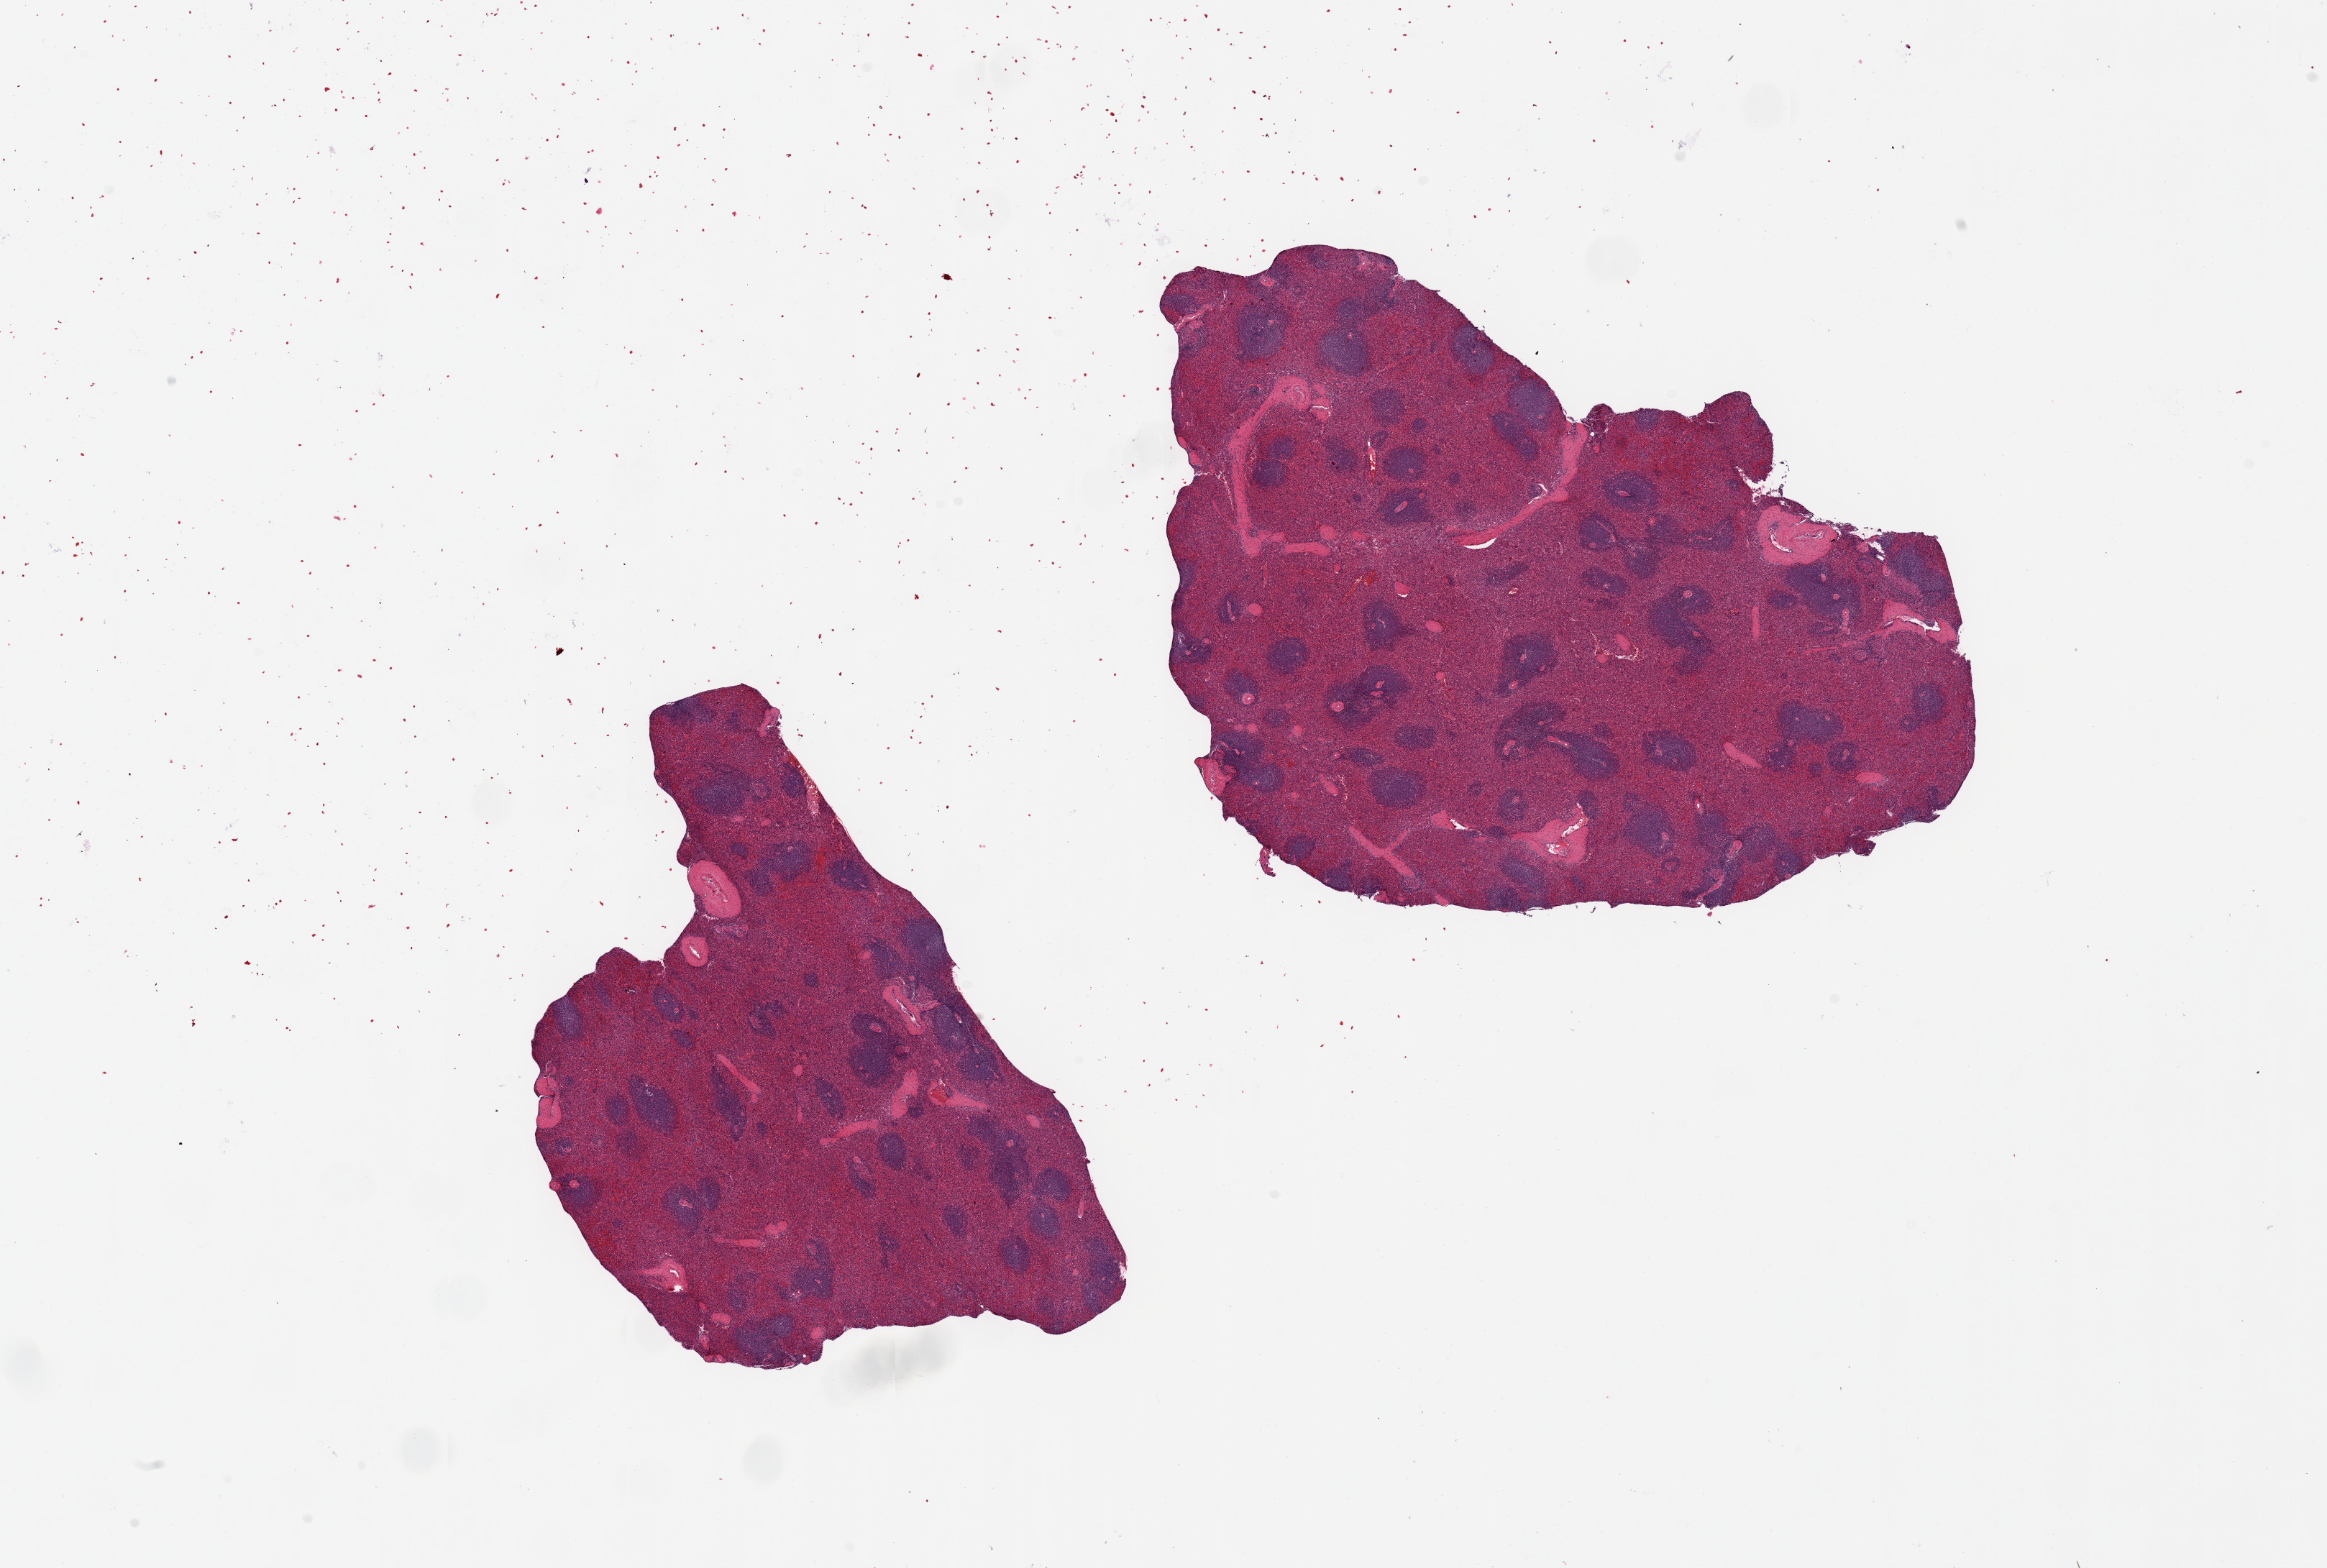
H&E whole-slide image — whole scanned area (about 25.6 x 17.3 mm) shown as a low-resolution overview, PAXgene-fixed, paraffin-embedded tissue, target tissue: spleen, tissue donor sample. Donor: male.
Pathologist's review note for this sample: 2 pieces, 8x5 & 10x7mm; Good red and white pulp.